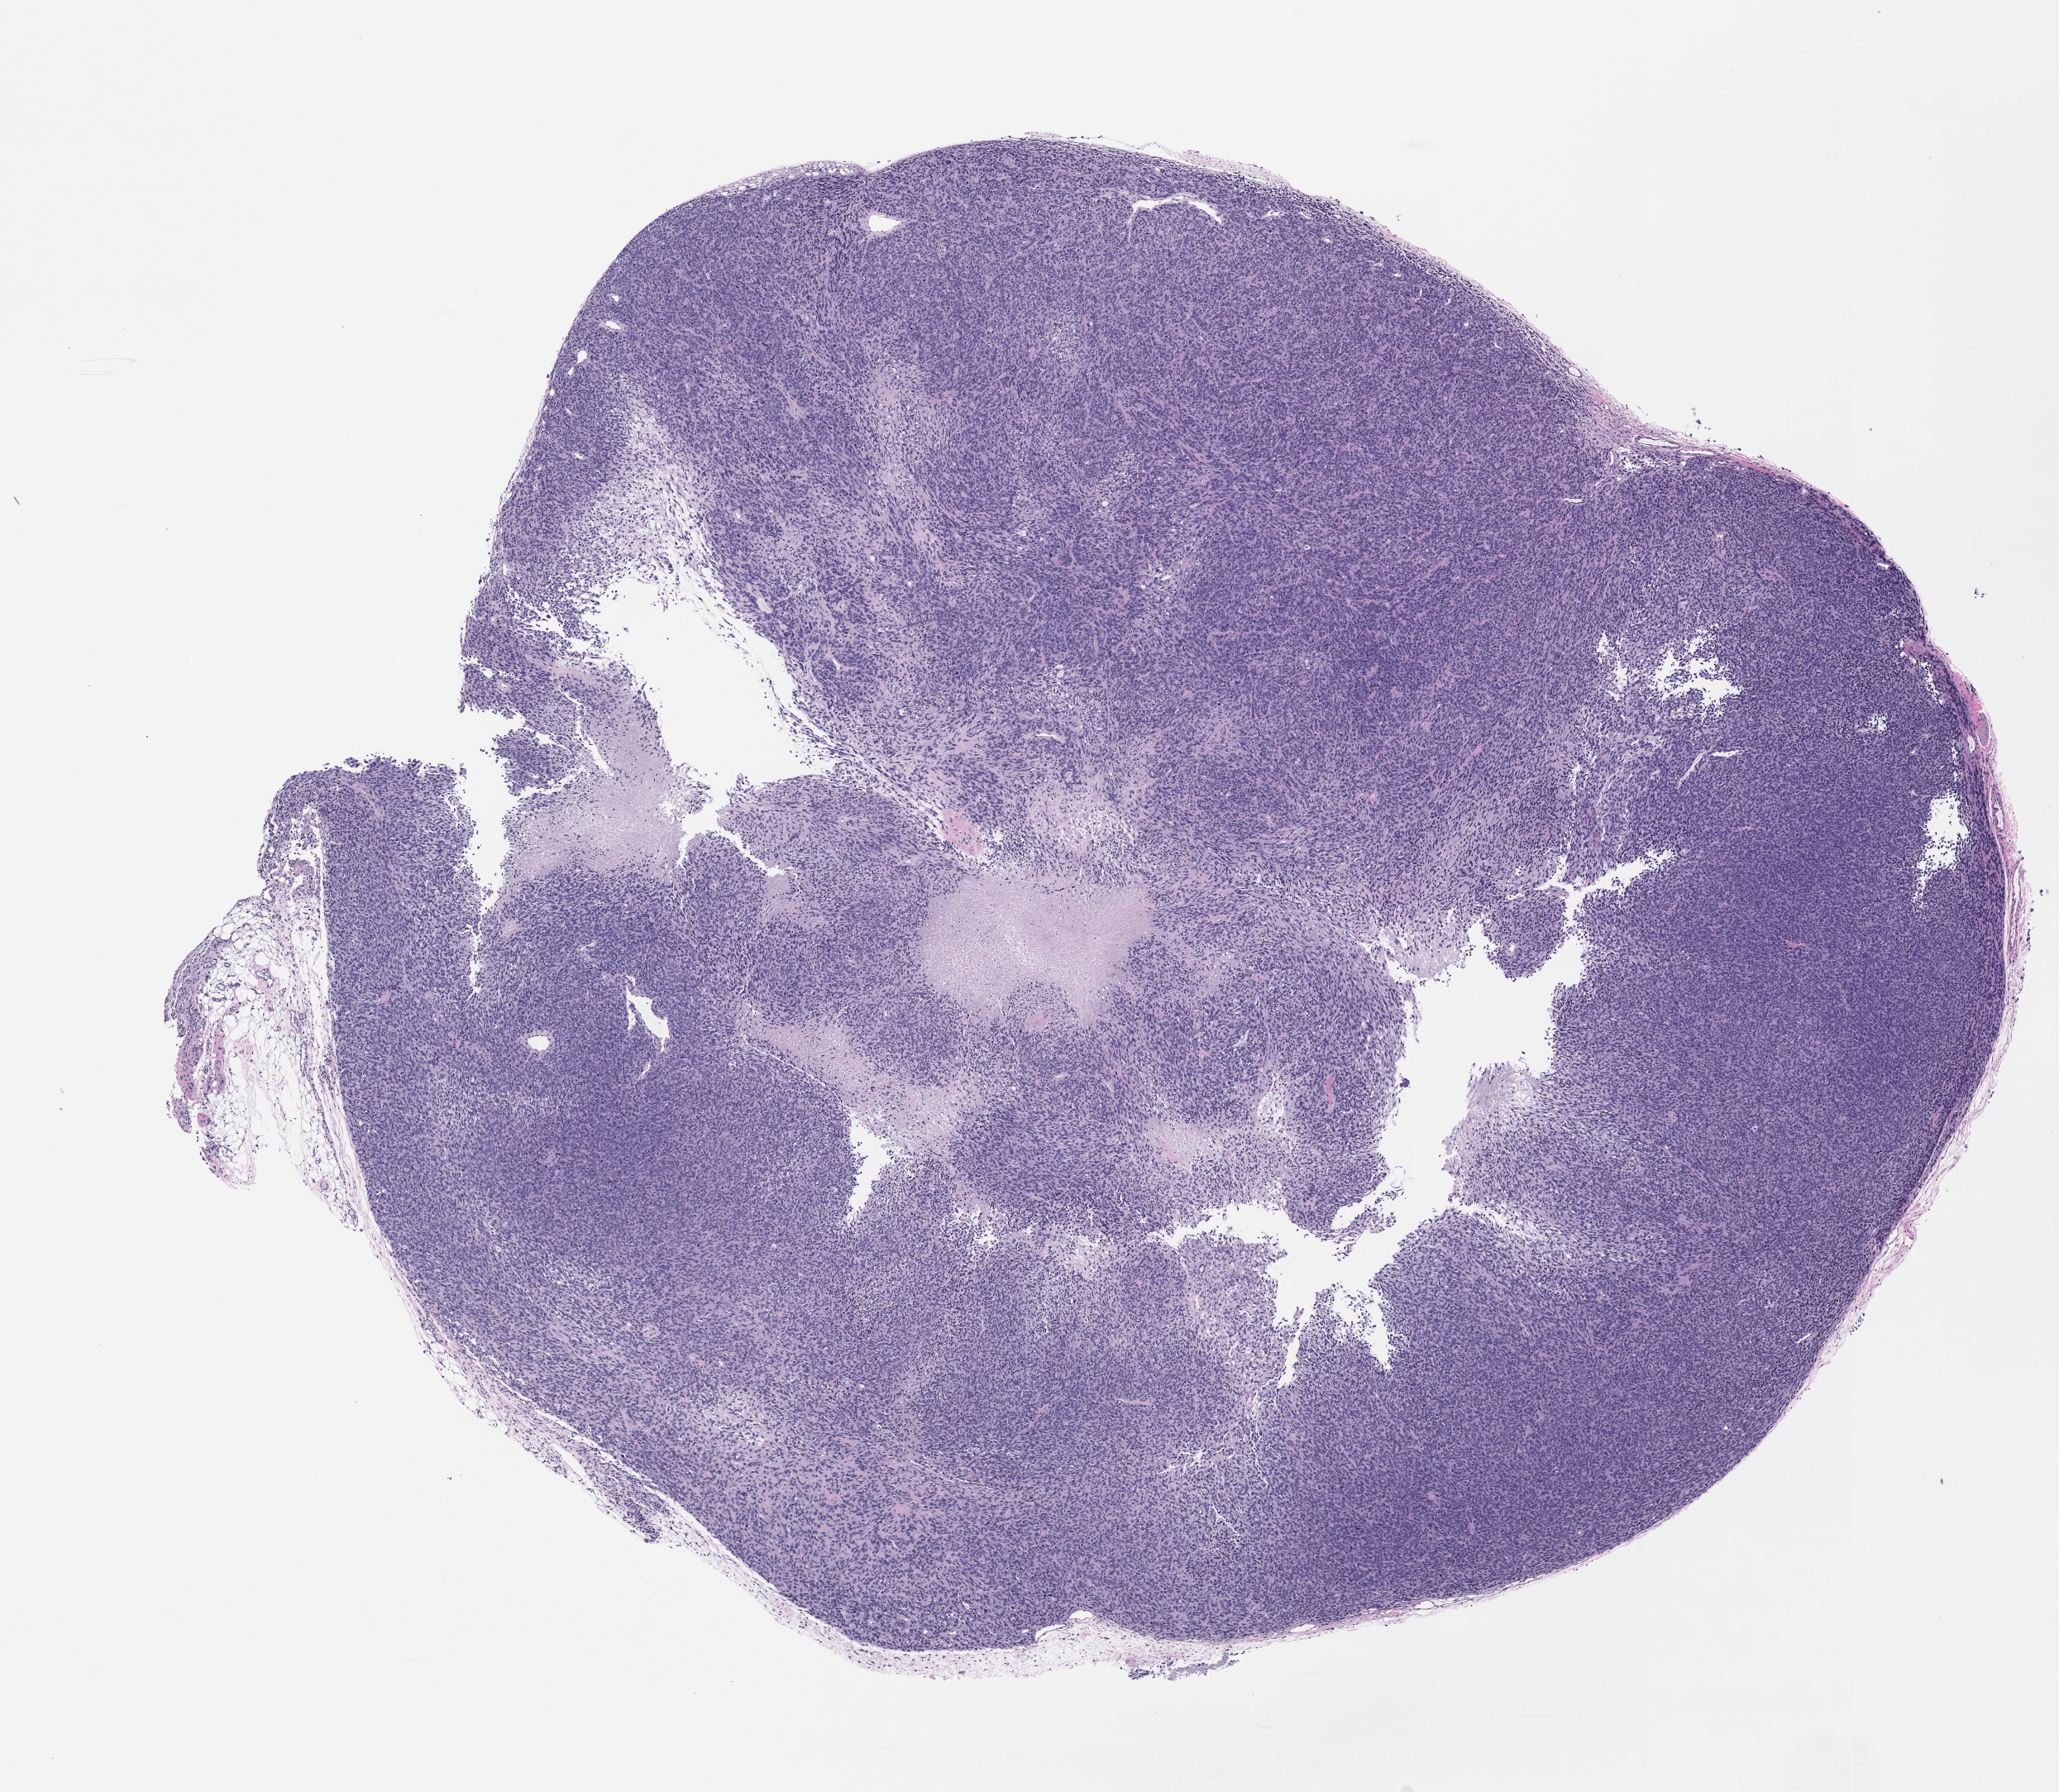
Whole-slide image, H&E: patient-derived xenograft (human tumor grown in a mouse), passage 1, a low-resolution overview of the entire scanned area, about 10.0 x 8.7 mm. Formalin-fixed paraffin-embedded section. Originating tumor site category: musculoskeletal.
Originating patient diagnosis: Spindle Cell Sarcoma.